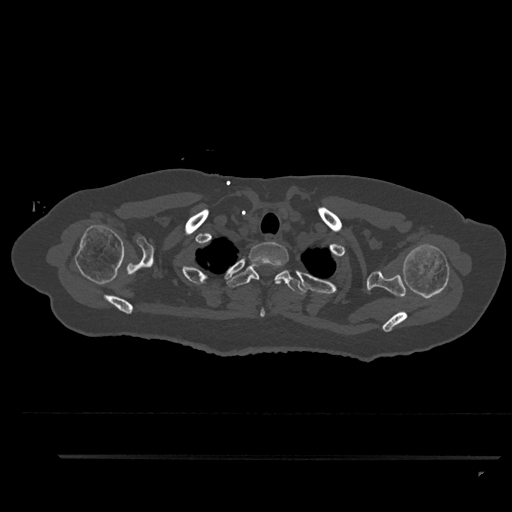
CT including the spine, one axial slice. Slice 739 of 797 in the series (ordered by position). Reconstruction kernel Br40s/3. Bone window (W 1800 / L 400 HU). 512 × 512 image matrix, field of view 408 × 408 mm. Patient: female, 44 years. Case-level facts recorded for this patient, not image findings: primary cancer: renal; vertebrae with lytic lesions (as recorded): L1.
Structures marked on this image (semi-automatic segmentation, software-assisted and operator-edited):
- T1 vertebra: bounding box [x1, y1, x2, y2] px = [249, 242, 289, 317]
- T2 vertebra: [227, 264, 306, 295]